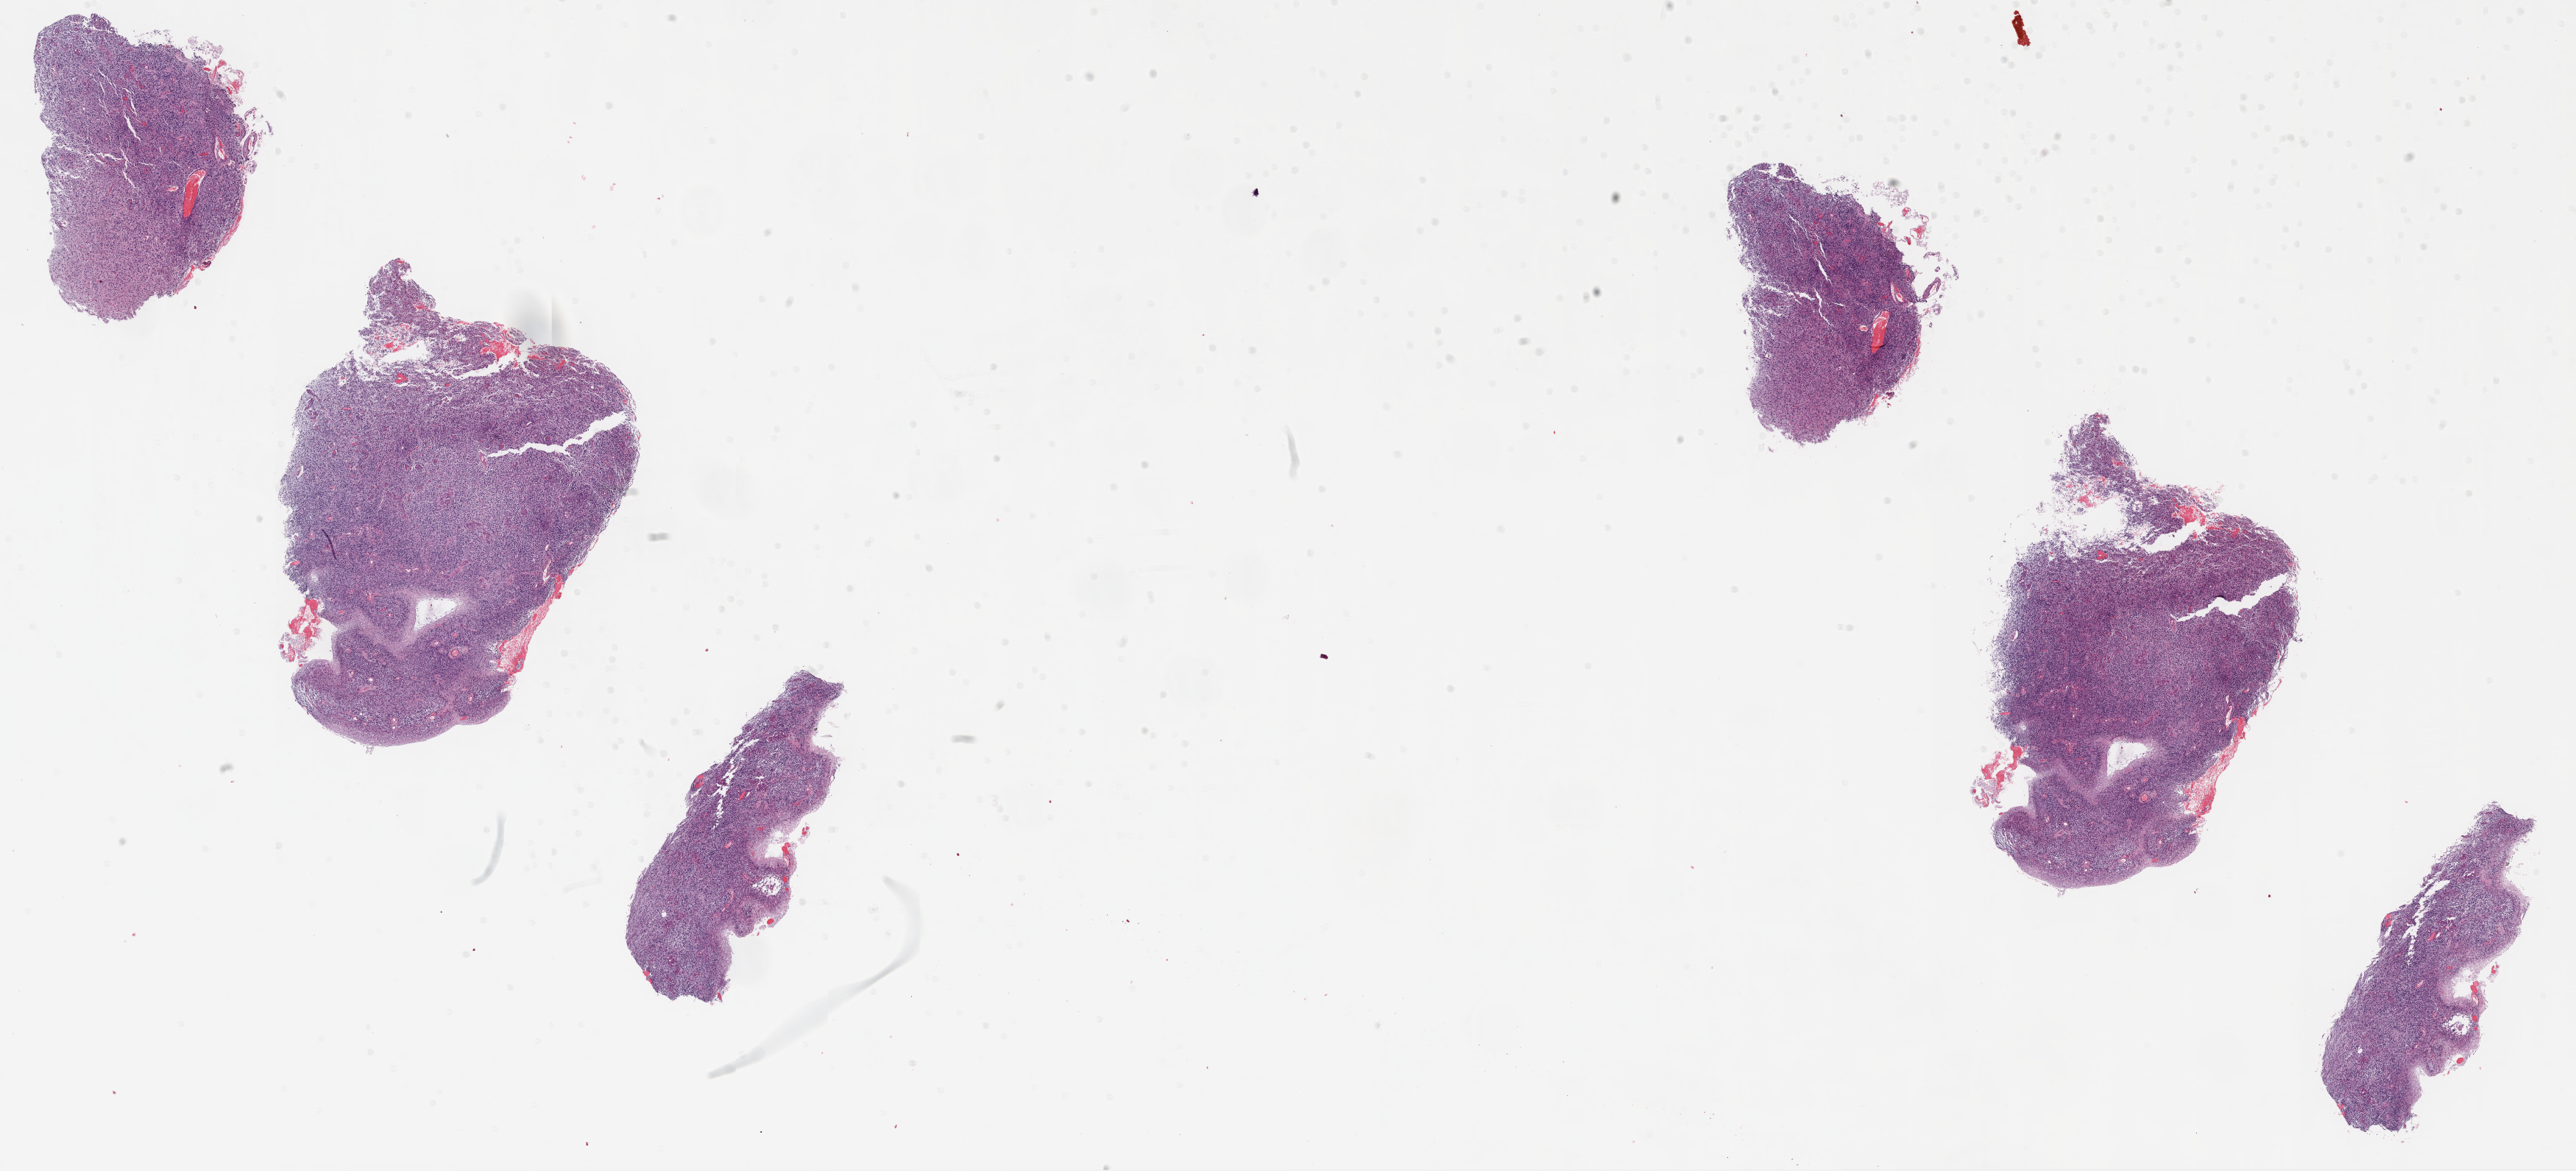
Digitized H&E tissue section (whole slide) — a low-resolution overview of the entire scanned area, about 28.1 x 12.8 mm (from a 20x scan). Formalin-fixed paraffin-embedded (FFPE) diagnostic section. Brain, primary tumour sample. Male patient; age at initial diagnosis 70 years.
Diagnosis: Glioblastoma.